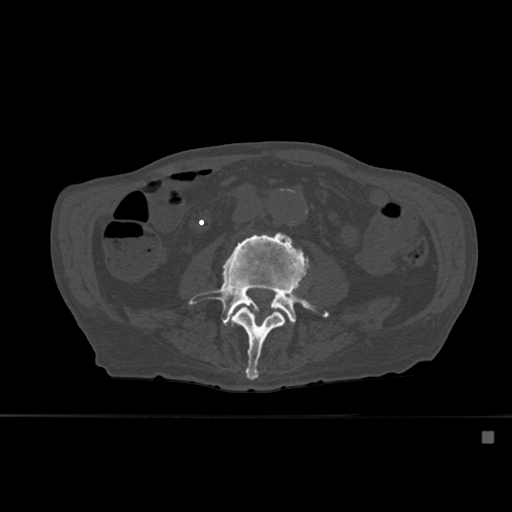
CT including the spine, one axial slice; slice 203 of 527 in the series (ordered by position); bone window (W 1800 / L 400 HU); 1.5 mm slice thickness; 512 × 512 image matrix, field of view 373 × 373 mm. Male patient, age 78 years. From the clinical record (not read from this slice): primary cancer: prostate.
Annotated regions visible in this slice (semi-automatic segmentation, software-assisted and operator-edited):
- L3 vertebra: box from (x=224, y=293) to (x=295, y=380) px
- L4 vertebra: (x=190, y=232)–(x=329, y=324)